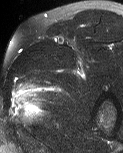
MRI of an extremity soft-tissue mass, one axial slice. Position 45 of 60 along the scan axis. T2-weighted fat-saturated. MR volume resampled by the dataset authors to the PET/CT grid (not the native acquisition matrix). 3.27 mm slice thickness. 123 × 153 image matrix, field of view 120 × 149 mm. Male patient. From the clinical record (not read from this slice): histological type: pleiomorphic liposarcoma; grade: high; site of the primary tumour: left thigh.
Outlined on this slice (expert contour drawn on MRI and transferred to this co-registered scan by the dataset authors):
- gross tumour volume including surrounding oedema: box from (x=11, y=82) to (x=46, y=124) px